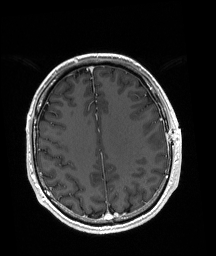
Brain MRI from a brain-tumour surgery series, one axial slice; position 66 of 192 along the scan axis; T1-weighted post-contrast; 1 mm slice thickness; 216 × 256 image matrix. From the clinical record (not read from this slice): histopathology: Astrocytoma; WHO grade: 3; IDH mutation: yes; tumour location: Left Posterior Frontal.
Structures marked on this image (outlined manually by an expert reader):
- tumour: bounding box (x1, y1, x2, y2) in pixels: (145, 130, 163, 150)